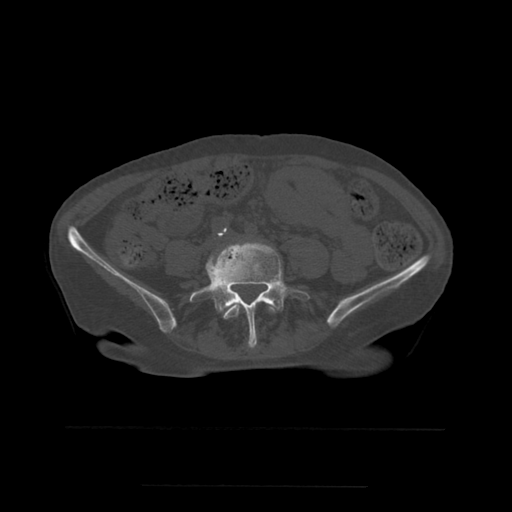
CT including the spine, one axial slice. Position 152 of 544 along the scan axis. Bone window (W 1800 / L 400 HU). 512 × 512 image matrix, field of view 350 × 350 mm. Patient age 58 years. Case-level facts recorded for this patient, not image findings: primary cancer: lung.
Structures marked on this image (semi-automatic segmentation, software-assisted and operator-edited):
- L4 vertebra: box from (x=212, y=250) to (x=275, y=320) px
- L5 vertebra: (x=190, y=243)–(x=302, y=348)